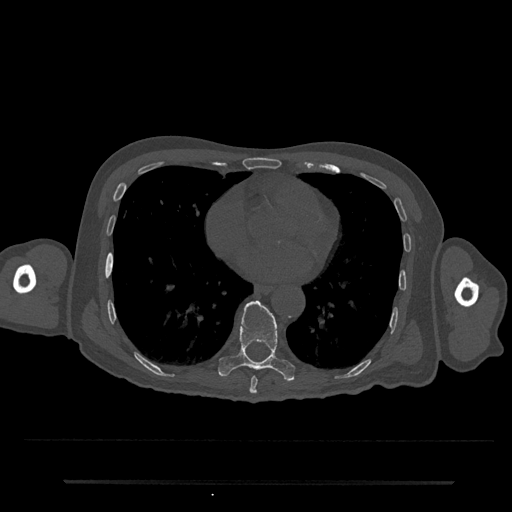
CT including the spine, one axial slice; slice 374 of 797 in the series (ordered by position); reconstruction kernel Br40s/3; bone window (W 1800 / L 400 HU); 0.5 mm slice thickness; 512 × 512 image matrix. Patient: male, 74 years. Case-level facts recorded for this patient, not image findings: primary cancer: prostate.
Outlined on this slice (semi-automatic segmentation, software-assisted and operator-edited):
- T8 vertebra: bounding box [x1, y1, x2, y2] px = [249, 376, 258, 394]
- T9 vertebra: [218, 301, 295, 381]